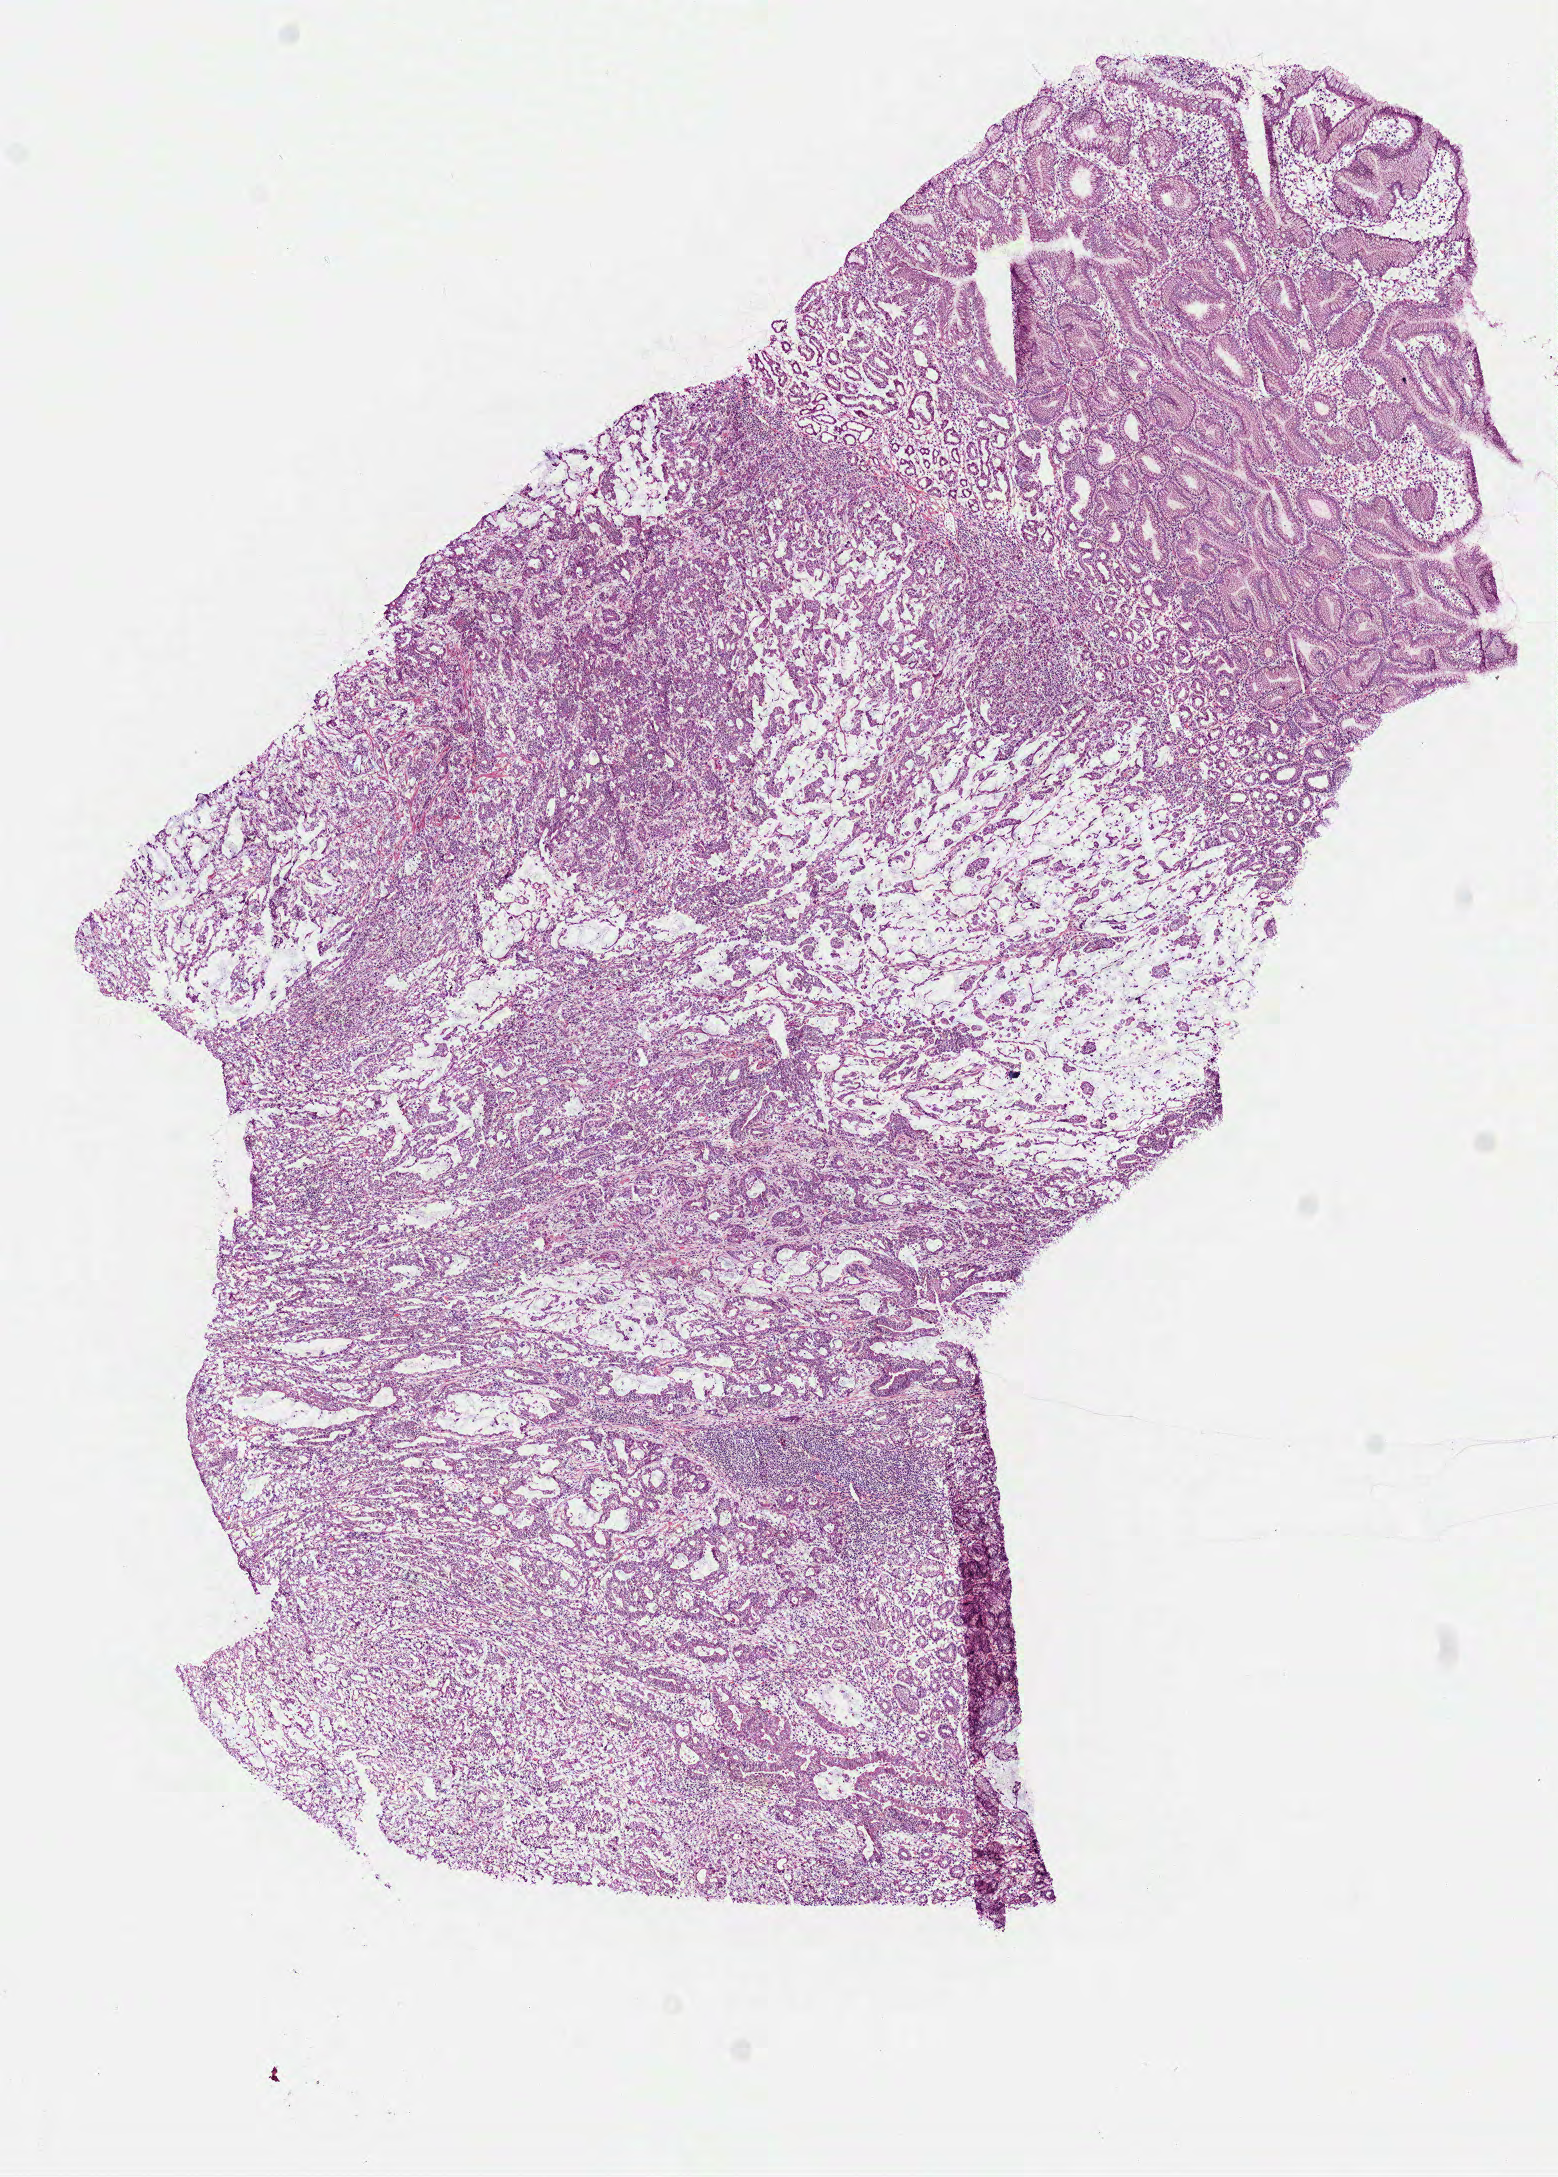
Whole-slide histology image, Hematoxylin and eosin (H&E) stained — whole scanned area (about 6.3 x 8.8 mm, slide scanned at 40x) shown as a low-resolution overview; frozen section from the bottom of the tissue portion; primary tumour sample from the stomach. Male patient.
Diagnosis: Mucinous adenocarcinoma (gastric antrum).